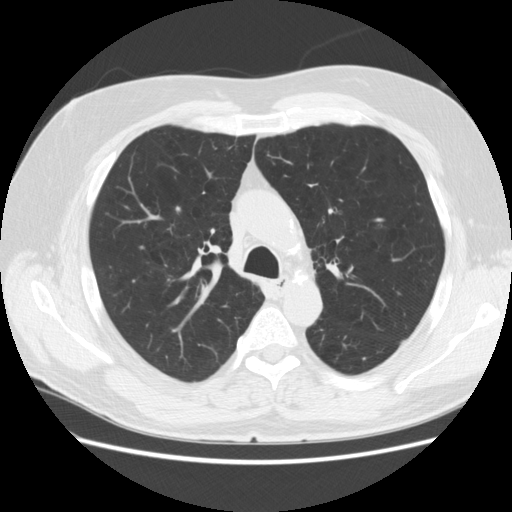
Axial slice from a low-dose chest CT screening exam. First (baseline) screen. Lung window (W 1500 / L -600 HU). 120 kVp. Slice 62 of 186 in the series. 512 × 512 image matrix. Male participant, aged 63 years at enrolment. Former smoker at enrolment.
- Lesion marked by an expert reader, bounding box (x1, y1, x2, y2) in pixels: (163, 198, 196, 224).
- Screening reader's record for this exam: no non-calcified nodule ≥4 mm recorded.
- Lung cancer was diagnosed 1085 days after this screen: adenocarcinoma, NOS, right upper lobe, stage IIA (AJCC 6th edition), 8 mm at pathology.